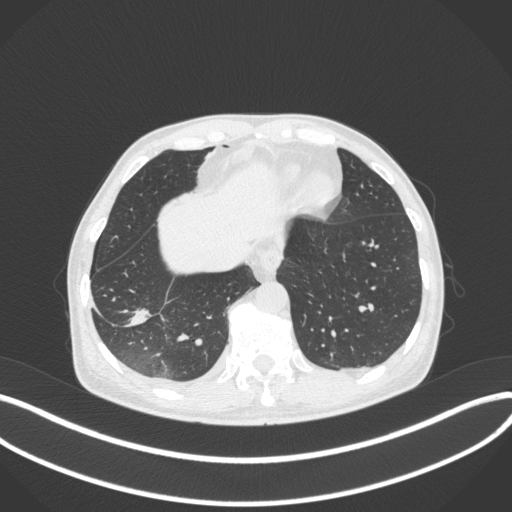
Chest CT, one axial slice. Position 84 of 385 along the scan axis. Reconstruction kernel B31f. 120 kVp. Lung window (W 1500 / L -600 HU). 512 × 512 image matrix, field of view 400 × 400 mm. Male patient, age 64 years. Case-level facts recorded for this patient, not image findings: clinical TNM (as recorded): T3 N0 M0; histopathological grade: G2-3.
Annotated regions visible in this slice (bounding box drawn by a radiologist):
- lung tumour (recorded histology: adenocarcinoma): bounding box <122,296,148,332> (left, top, right, bottom; pixels)